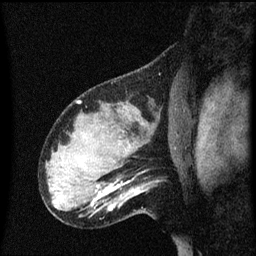
Breast MRI (dynamic contrast-enhanced), one sagittal slice. Slice 44 of 60 in the series (ordered by position). Dynamic contrast-enhanced series, image 2 of 3 at this slice position (ordered by acquisition). 1.5 T. TE 4.2 ms, TR 8.4 ms. 256 × 256 image matrix, field of view 200 × 200 mm. Female patient, age 31 years. From the clinical record (not read from this slice): setting: breast cancer imaged before/during neoadjuvant chemotherapy; receptor status: HR-positive, HER2-negative.
Outlined on this slice (semi-automatically segmented with operator editing):
- analysis volume of interest (the breast-tissue region the enhancement analysis was run in; not a lesion): bounding box [x1, y1, x2, y2] px = [102, 166, 159, 217]
- tumour enhancement mask (voxels above the 70 % enhancement threshold inside the analysis volume of interest): [107, 182, 129, 211]